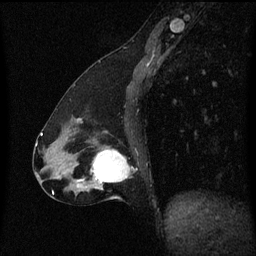
Breast MRI (dynamic contrast-enhanced), one sagittal slice; slice 25 of 60 in the series (ordered by position); dynamic contrast-enhanced series, image 2 of 3 at this slice position (ordered by acquisition); 1.5 T; TE 4.2 ms, TR 8.4 ms; 2 mm slice thickness; 256 × 256 image matrix, field of view 200 × 200 mm. Female patient, age 47 years.
Structures marked on this image (semi-automatically segmented with operator editing):
- analysis volume of interest (the breast-tissue region the enhancement analysis was run in; not a lesion): bounding box (x1, y1, x2, y2) in pixels: (81, 144, 130, 193)
- tumour enhancement mask (voxels above the 70 % enhancement threshold inside the analysis volume of interest): (81, 150, 130, 185)